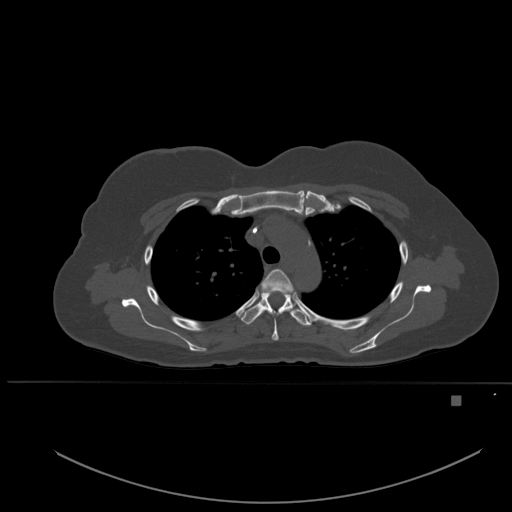
CT including the spine, one axial slice; slice 385 of 651 in the series (ordered by position); bone window (W 1800 / L 400 HU); 1.5 mm slice thickness; 512 × 512 image matrix. Female patient, age 49 years. Case-level facts recorded for this patient, not image findings: primary cancer: breast.
Outlined on this slice (semi-automatically segmented with operator editing):
- T3 vertebra: bounding box (x1, y1, x2, y2) in pixels: (261, 269, 295, 341)
- T4 vertebra: (240, 291, 311, 326)